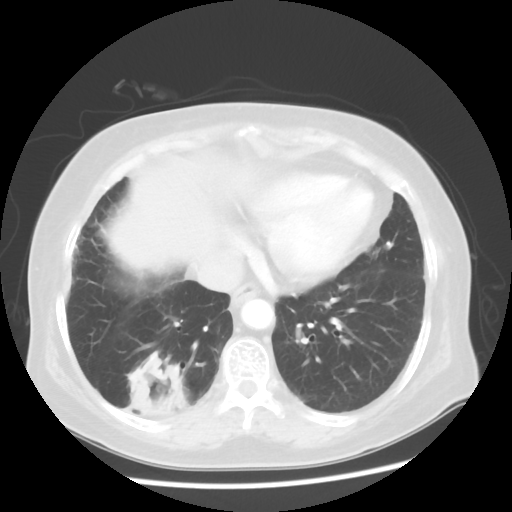
Chest CT, one axial slice. Slice 18 of 56 in the series (ordered by position). Reconstruction kernel STANDARD. 120 kVp. Lung window (W 1500 / L -600 HU). 5 mm slice thickness. 512 × 512 image matrix, field of view 360 × 360 mm. Patient: female, 64 years. Case-level facts recorded for this patient, not image findings: clinical TNM (as recorded): Tis N0 M0.
Structures marked on this image (bounding box drawn by a radiologist):
- lung tumour (recorded histology: adenocarcinoma): box from (x=125, y=349) to (x=189, y=428) px